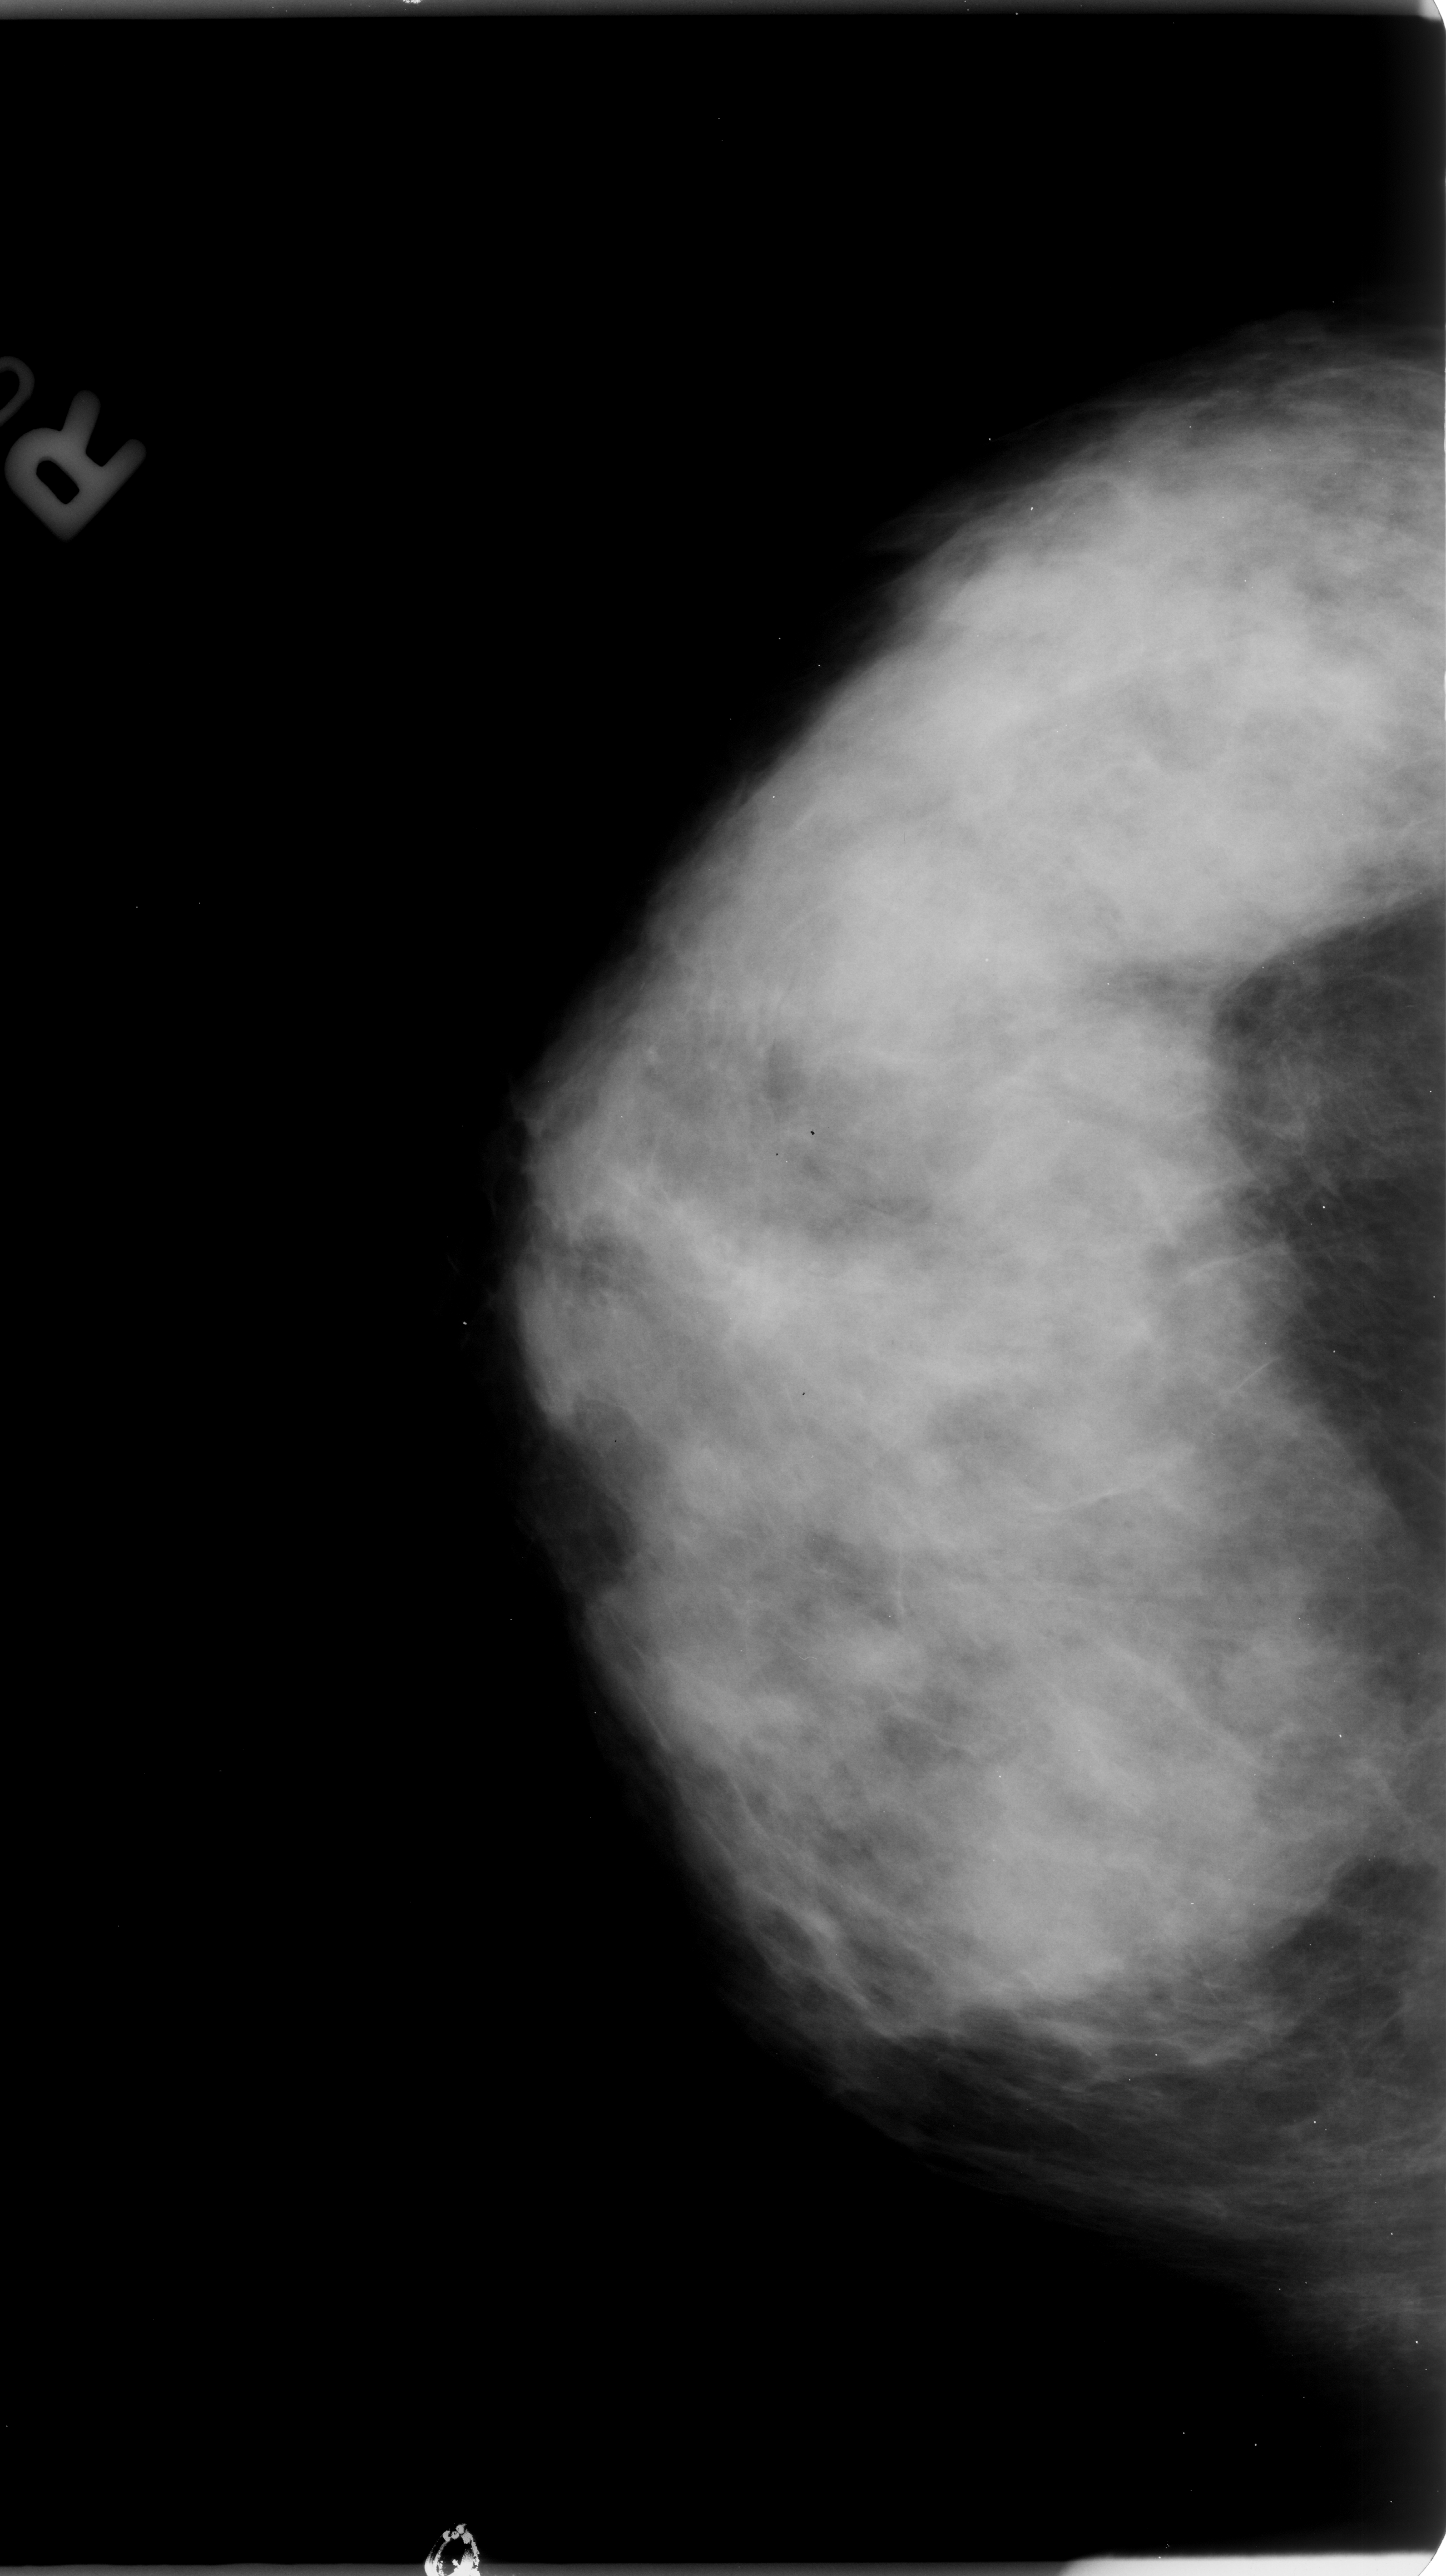
Digitized screen-film mammogram, right breast, craniocaudal (CC) view, BI-RADS breast density category 4 (scale 1–4).
Mass, shape round, margins circumscribed / obscured; BI-RADS assessment category 3; subtlety rating 2 on a 1 (subtle) to 5 (obvious) scale; pathology (as recorded): benign.